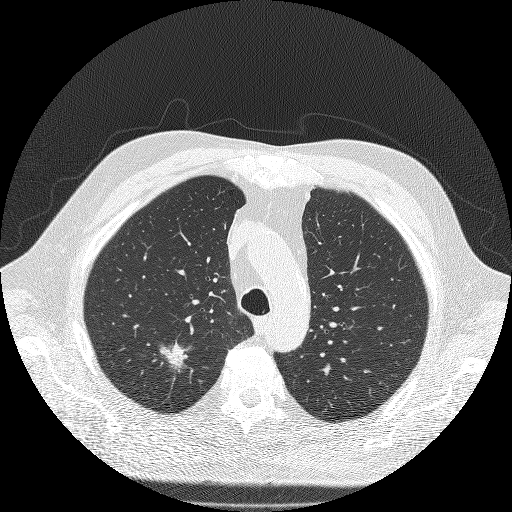
Axial slice from a low-dose chest CT screening exam. Second screening round (one year after baseline). Lung window (W 1500 / L -600 HU). Lung (sharp) reconstruction kernel (FC51). 120 kVp. Male, age 71 years at enrolment. Former smoker at enrolment.
Expert reader's lesion annotation, bounding box <138,327,204,389> (left, top, right, bottom; pixels). The screening reader recorded 3 non-calcified nodules or masses ≥4 mm on this exam; which of them this box marks is not recorded. Official screen result: positive, other. Lung cancer was diagnosed 59 days after this screen: bronchiolo-alveolar adenocarcinoma, NOS, right upper lobe, moderately differentiated (G2), stage IIIA (AJCC 6th edition), 25 mm at pathology.